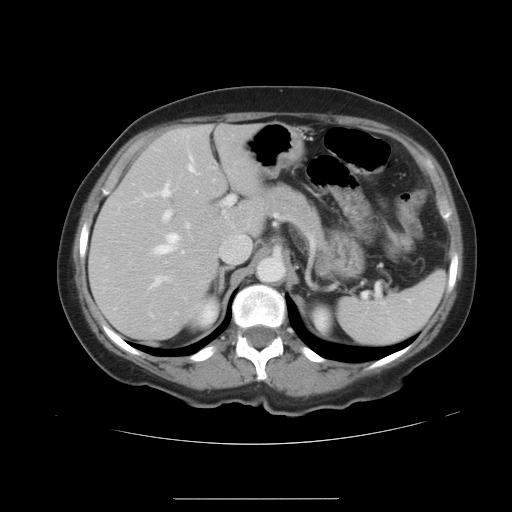
Contrast-enhanced abdominal CT, one axial slice. Position 25 of 41 along the scan axis. 120 kVp. Intravenous contrast given. Soft-tissue window (W 400 / L 40 HU). 5 mm slice thickness. 512 × 512 image matrix, field of view 381 × 381 mm. Female patient, age 63 years. From the clinical record (not read from this slice): diagnosis: colorectal cancer liver metastases, imaged before liver resection; multiple liver metastases: yes; largest metastasis: 1.5 cm; disease in both lobes: yes.
Structures marked on this image (outlined manually by an expert reader):
- hepatic veins: bounding box <154,158,194,279> (left, top, right, bottom; pixels)
- liver: <90,125,264,341>
- planned liver remnant (the part of the liver to remain after resection): <90,125,264,341>
- portal vein (with intrahepatic branches): <154,185,233,286>